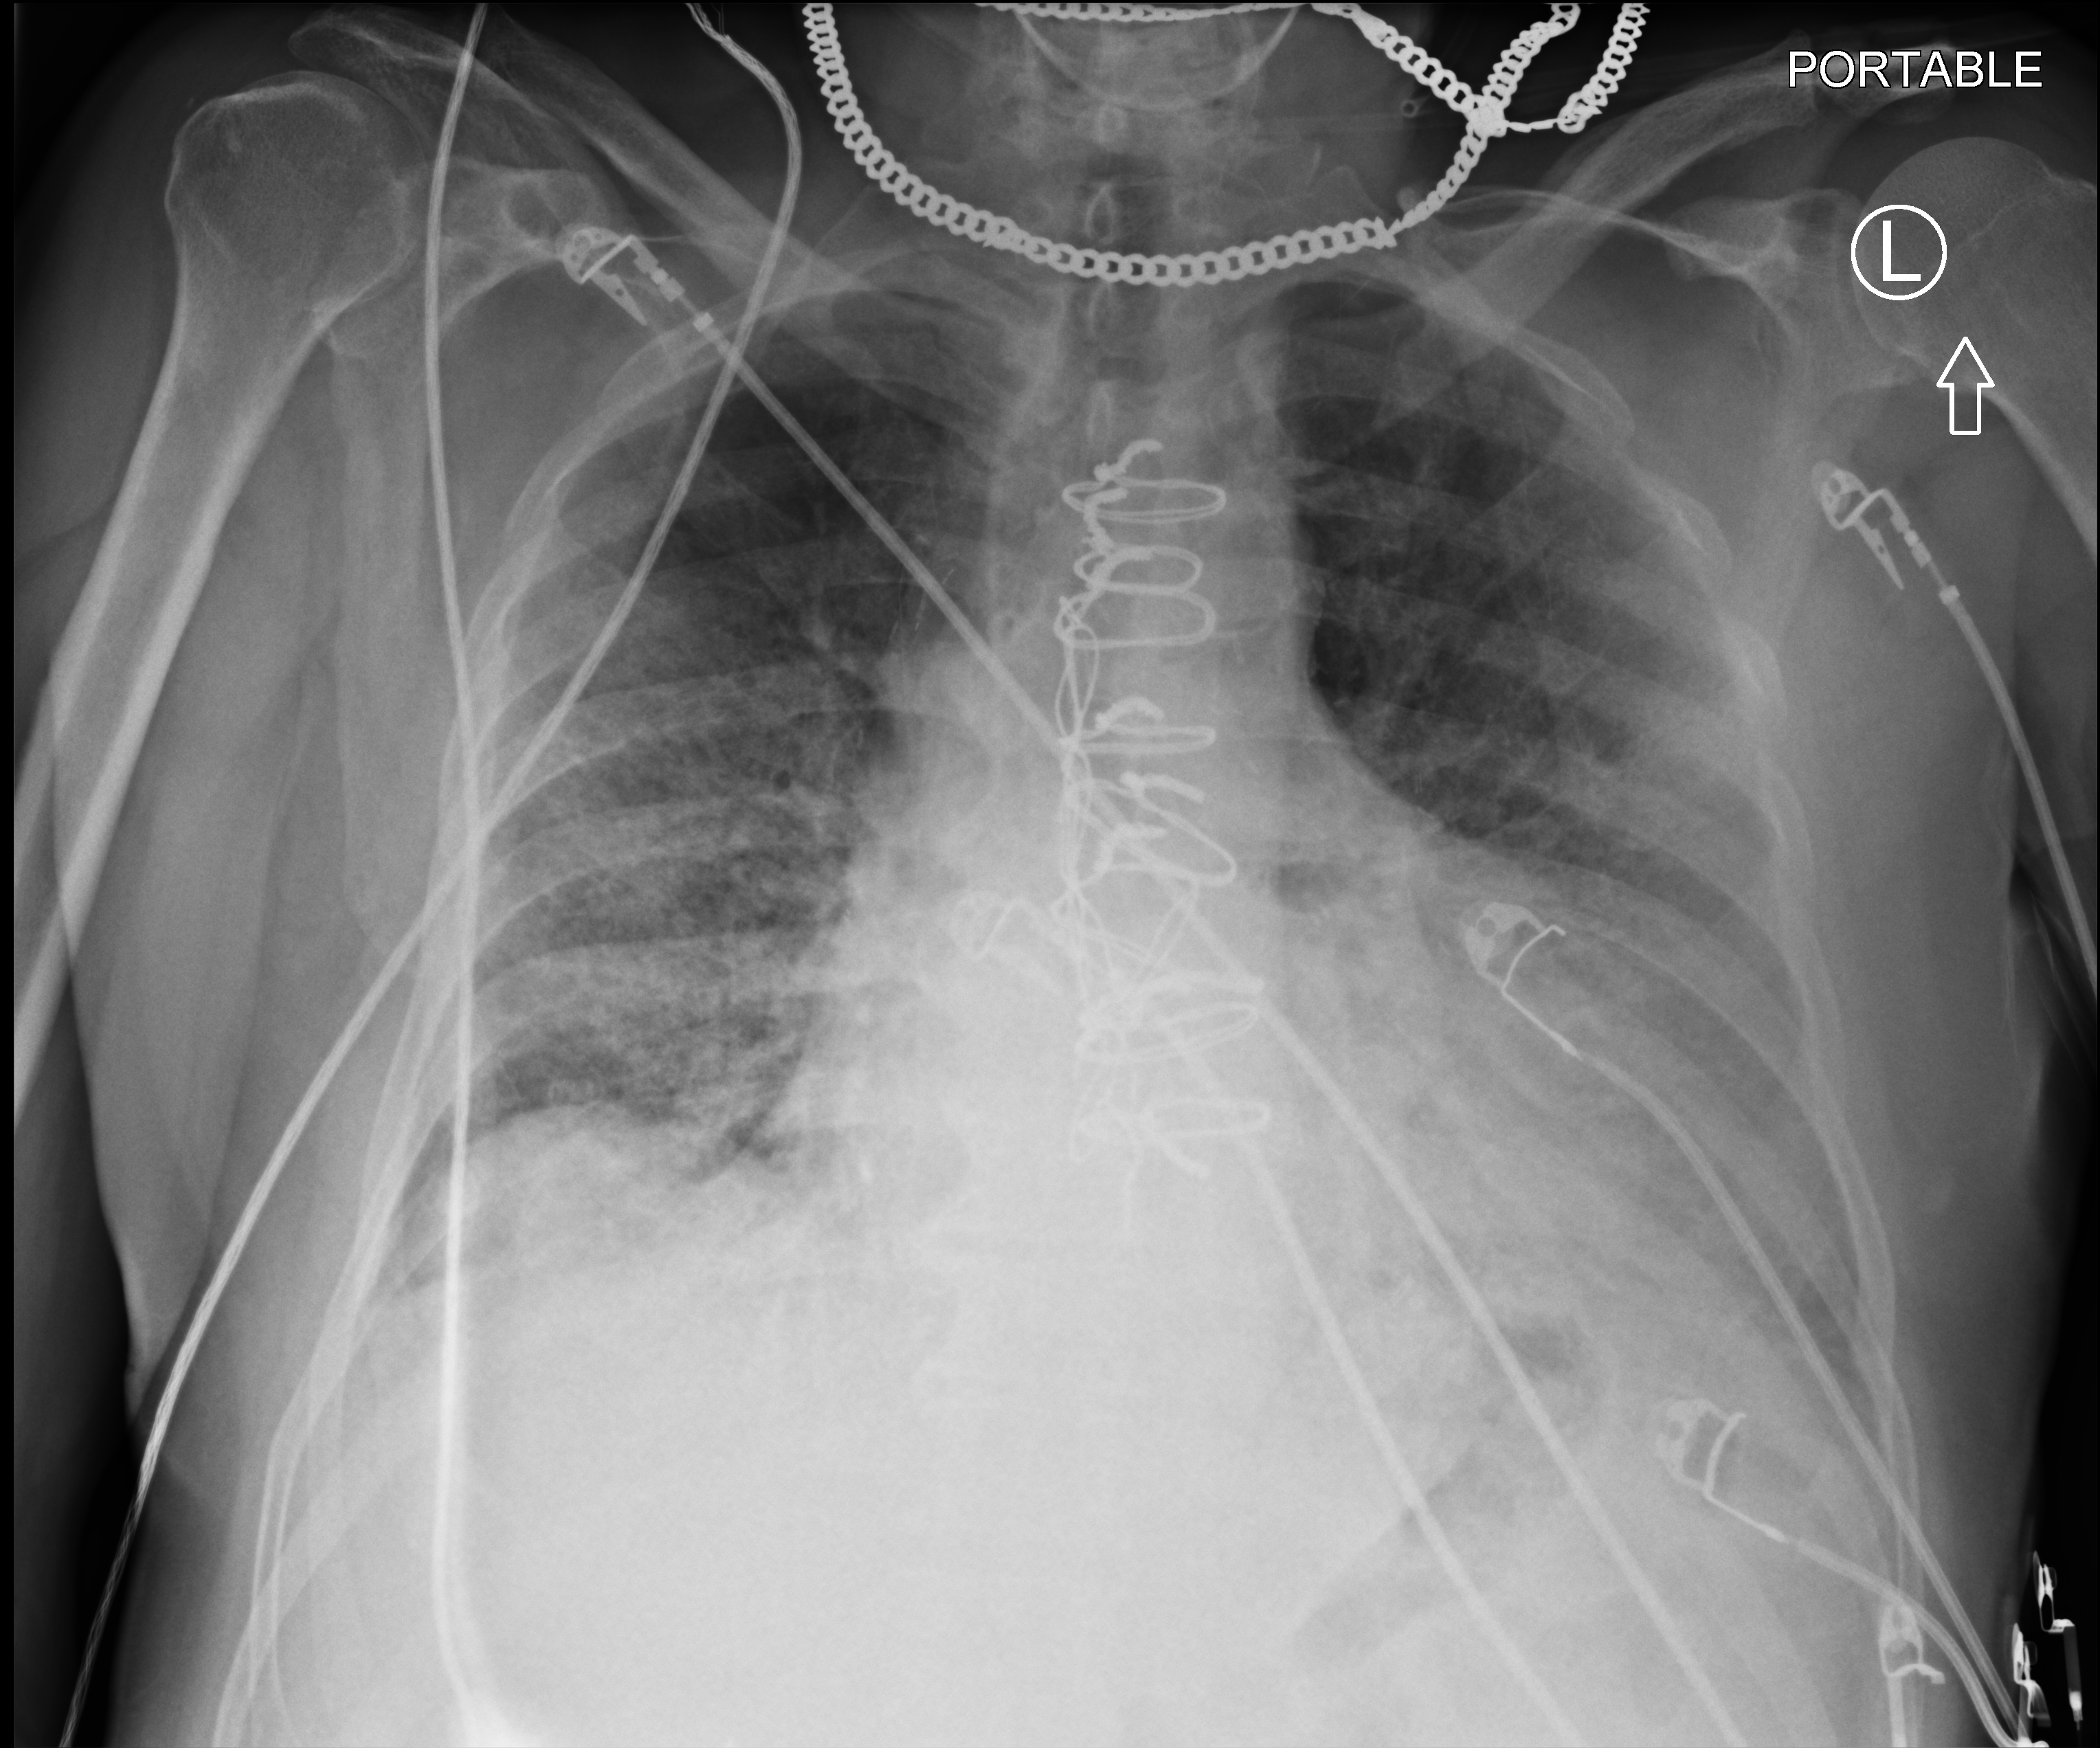
Chest X-ray (portable), anteroposterior (AP) projection. Patient hospitalised with COVID-19; male, aged 75–90 years.
From the hospital-stay record, not from the radiograph (when in the stay this image was taken is not recorded): admitted to intensive care during this hospital stay: no; mechanically ventilated during this hospital stay: yes.